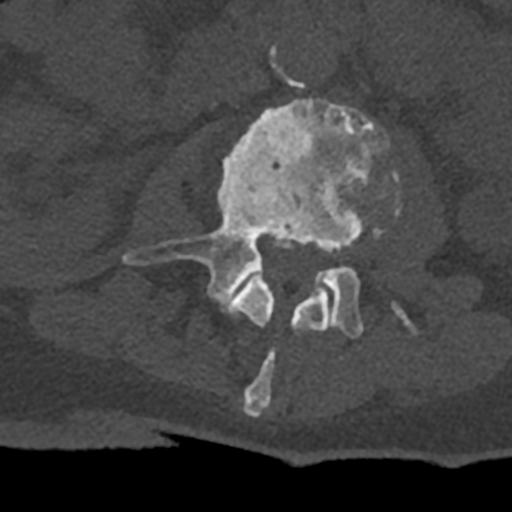
CT including the spine, one axial slice; position 342 of 797 along the scan axis; reconstruction kernel Br40s/3; 120 kVp; bone window (W 1800 / L 400 HU); 0.5 mm slice thickness; 512 × 512 image matrix, field of view 160 × 160 mm. Patient: male, 74 years. Case-level facts recorded for this patient, not image findings: primary cancer: renal; vertebrae with lytic lesions (as recorded): T10, L1, L2, L3, L4, L5.
Outlined on this slice (semi-automatically segmented with operator editing):
- L2 vertebra: box from (x=227, y=266) to (x=331, y=417) px
- L3 vertebra: (x=123, y=98)–(x=413, y=339)